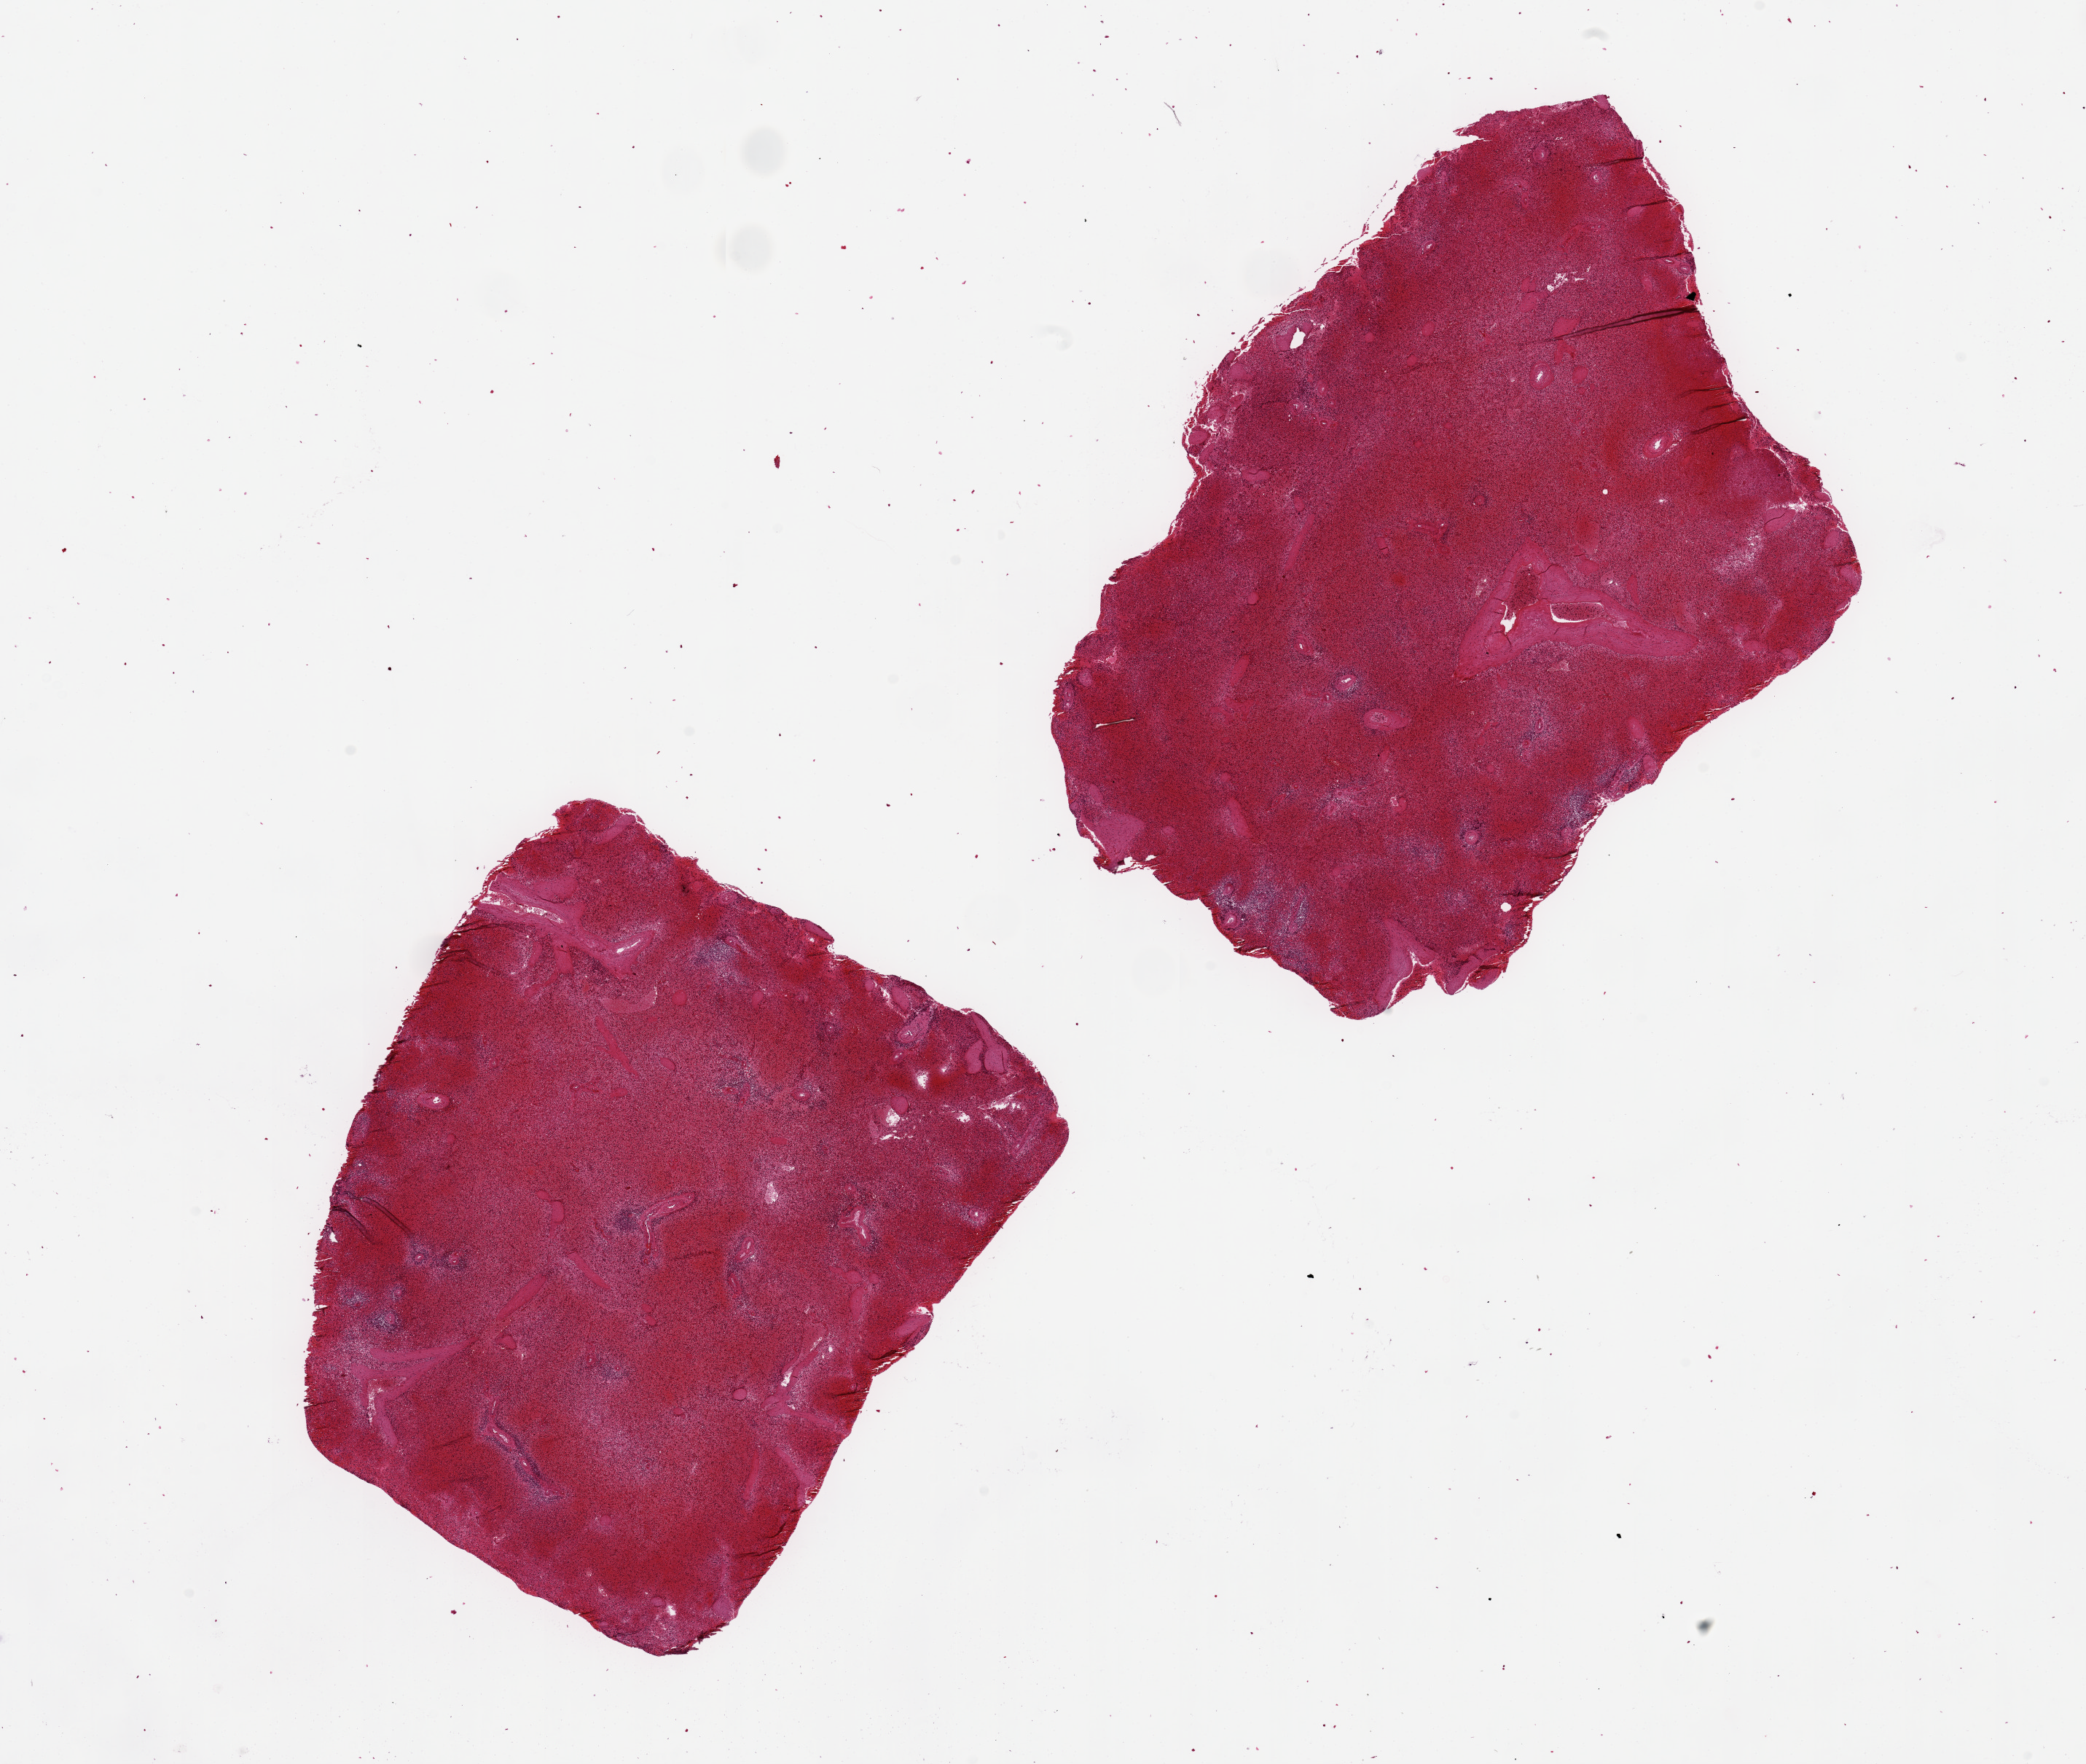
Digitized H&E-stained section — a low-resolution overview of the entire scanned area, about 22.6 x 19.1 mm (acquisition: 20x scan); PAXgene-fixed, paraffin-embedded tissue; target tissue: spleen; tissue donor sample. Donor: male.
Pathologist's review note for this sample: 2 pieces ~7xx7mm badly autolyzed.